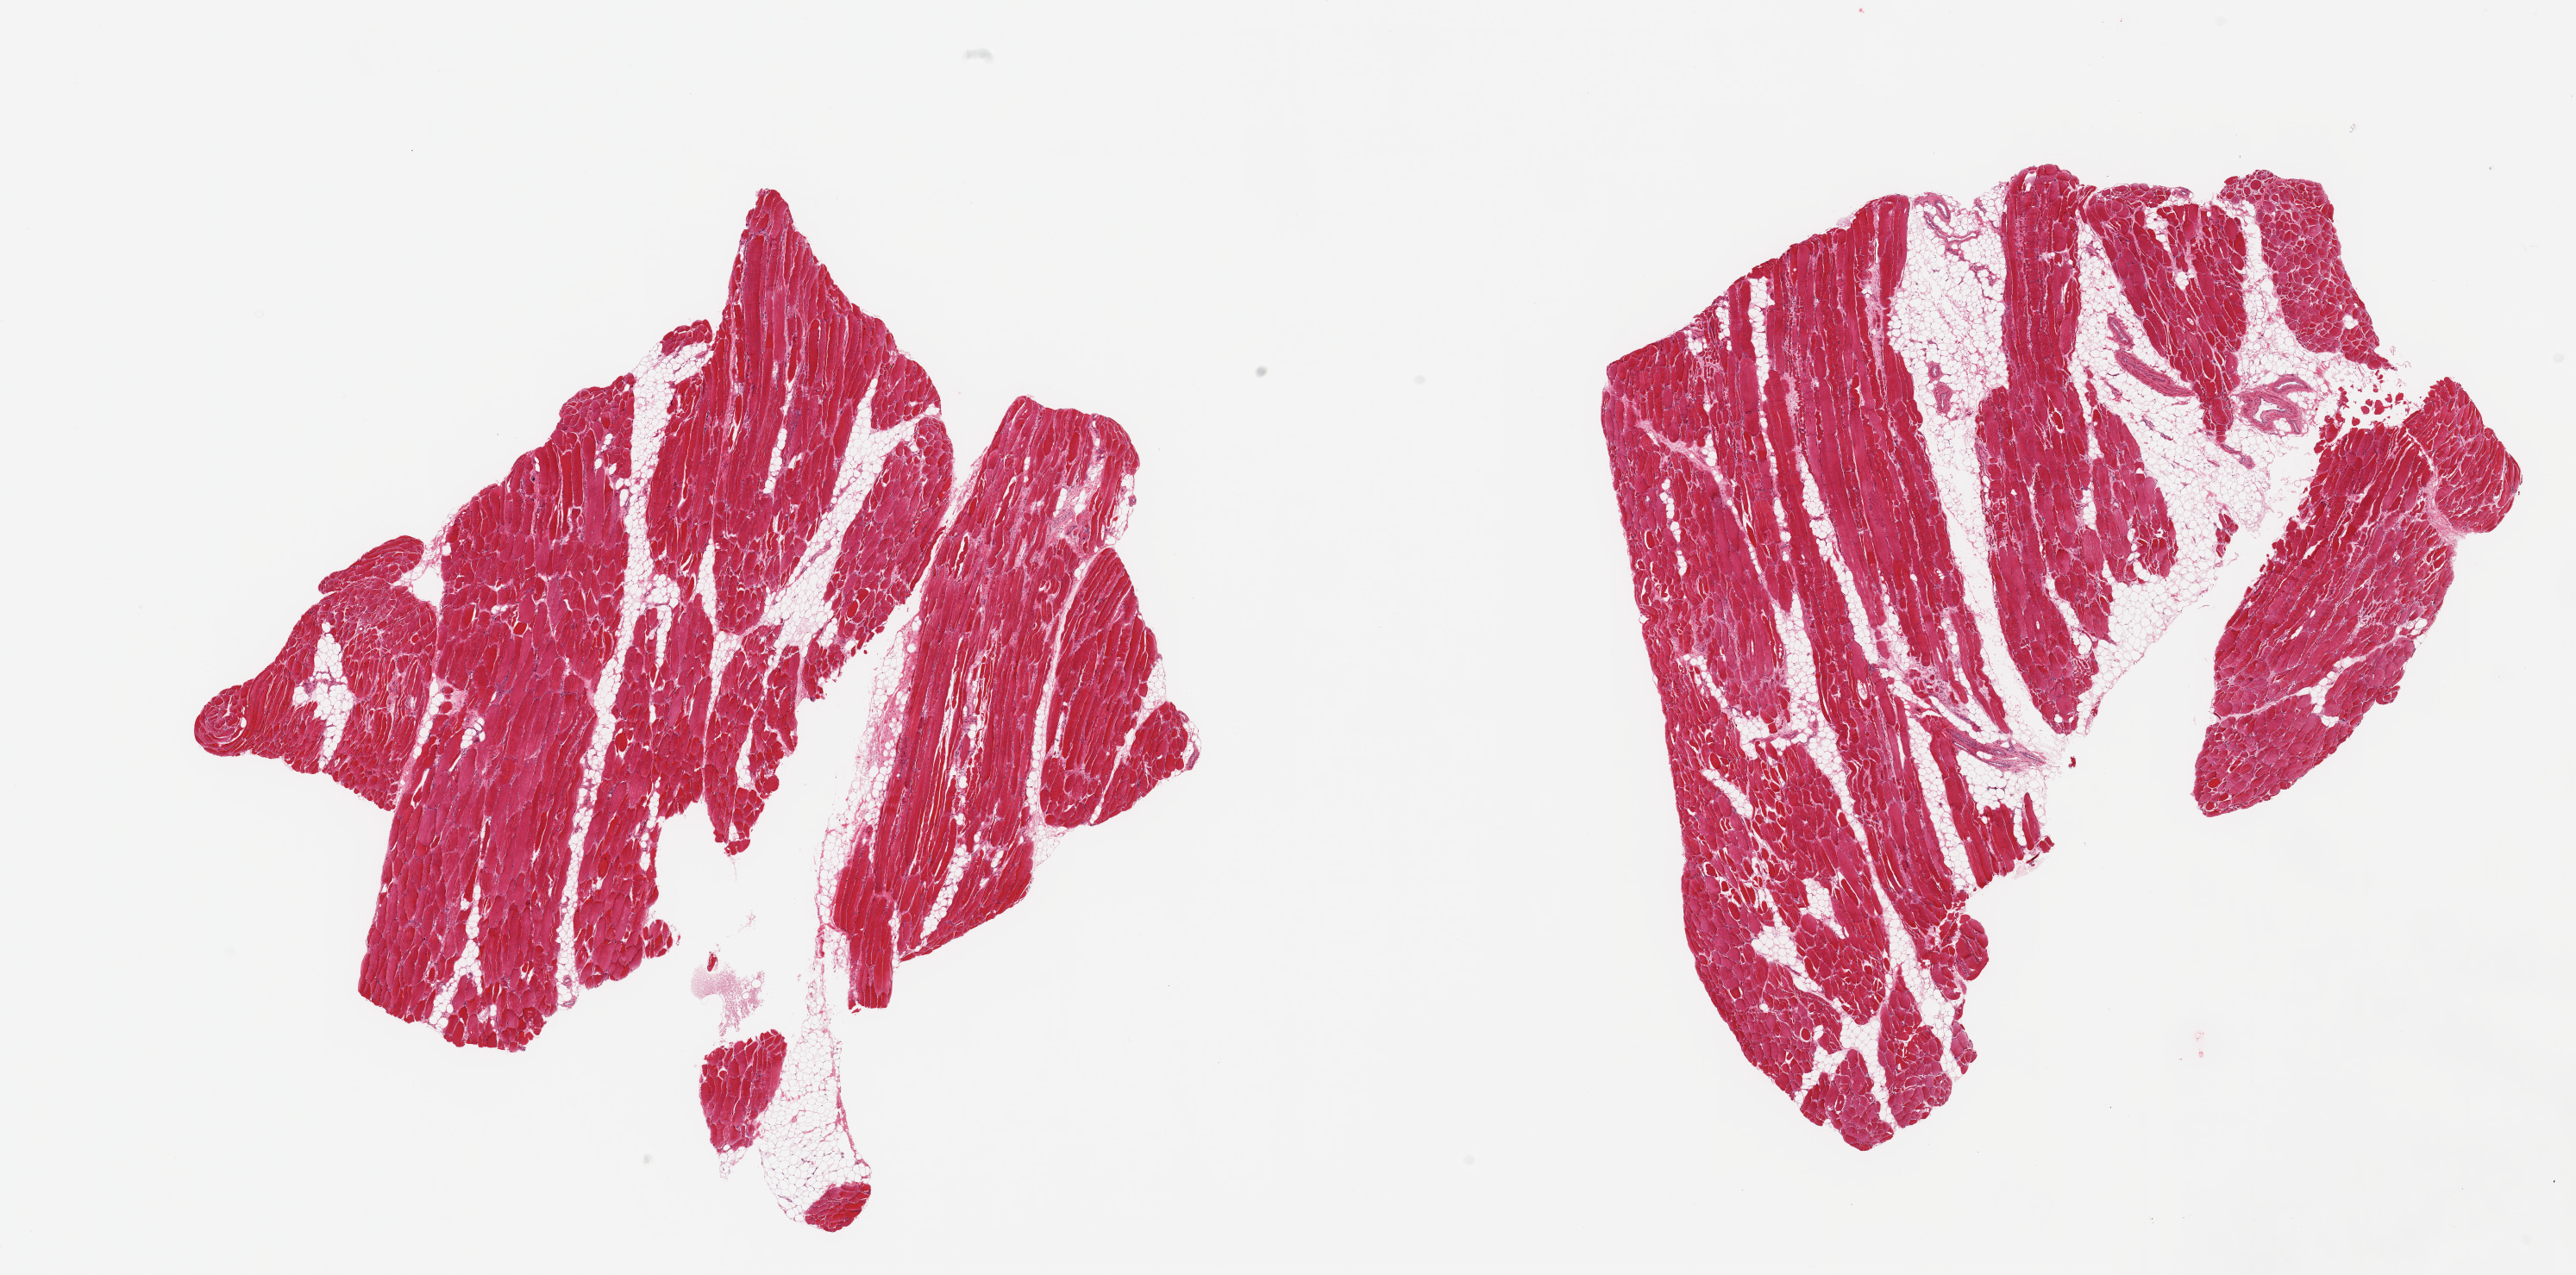
Whole-slide image, hematoxylin and eosin (H&E) stain, brightfield, shown as a low-resolution overview of the whole scanned area (about 23.6 x 11.7 mm, from a 20x scan); PAXgene-fixed, paraffin-embedded tissue; section of skeletal muscle (target tissue); tissue donor sample. Donor: female.
Reviewer comment on this tissue sample: 2 pieces; focal atrophy; 10% internal fat.